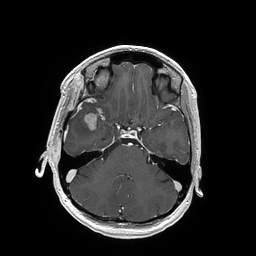
Brain MRI from a brain-tumour surgery series, one axial slice; position 117 of 202 along the scan axis; T1-weighted post-contrast; 256 × 256 image matrix, field of view 250 × 250 mm. From the clinical record (not read from this slice): histopathology: Glioblastoma; WHO grade: 4; IDH mutation: no; tumour location: Right Insular.
Outlined on this slice (outlined manually by an expert reader):
- tumour: bounding box (x1, y1, x2, y2) in pixels: (84, 109, 100, 130)